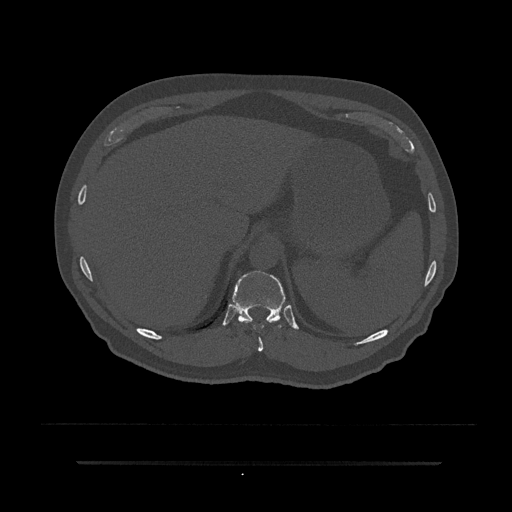
CT including the spine, one axial slice. Position 291 of 797 along the scan axis. Reconstruction kernel Br40s/3. 120 kVp. Bone window (W 1800 / L 400 HU). 512 × 512 image matrix, field of view 464 × 464 mm. Male patient, age 59 years. Case-level facts recorded for this patient, not image findings: primary cancer: bile ducts; vertebrae with lytic lesions (as recorded): T10.
Annotated regions visible in this slice (semi-automatic segmentation, software-assisted and operator-edited):
- T10 vertebra: bounding box [x1, y1, x2, y2] px = [234, 287, 277, 352]
- T11 vertebra: [231, 270, 286, 328]